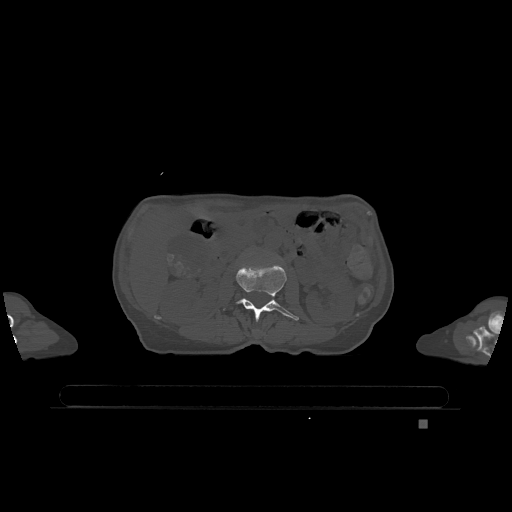
CT including the spine, one axial slice; position 412 of 1317 along the scan axis; bone window (W 1800 / L 400 HU); 512 × 512 image matrix, field of view 500 × 500 mm. Female patient, age 74 years. Case-level facts recorded for this patient, not image findings: primary cancer: lung; vertebrae with lytic lesions (as recorded): T1, T4, T5, T6, L4, L5.
Outlined on this slice (semi-automatically segmented with operator editing):
- L2 vertebra: box from (x=223, y=264) to (x=299, y=321) px